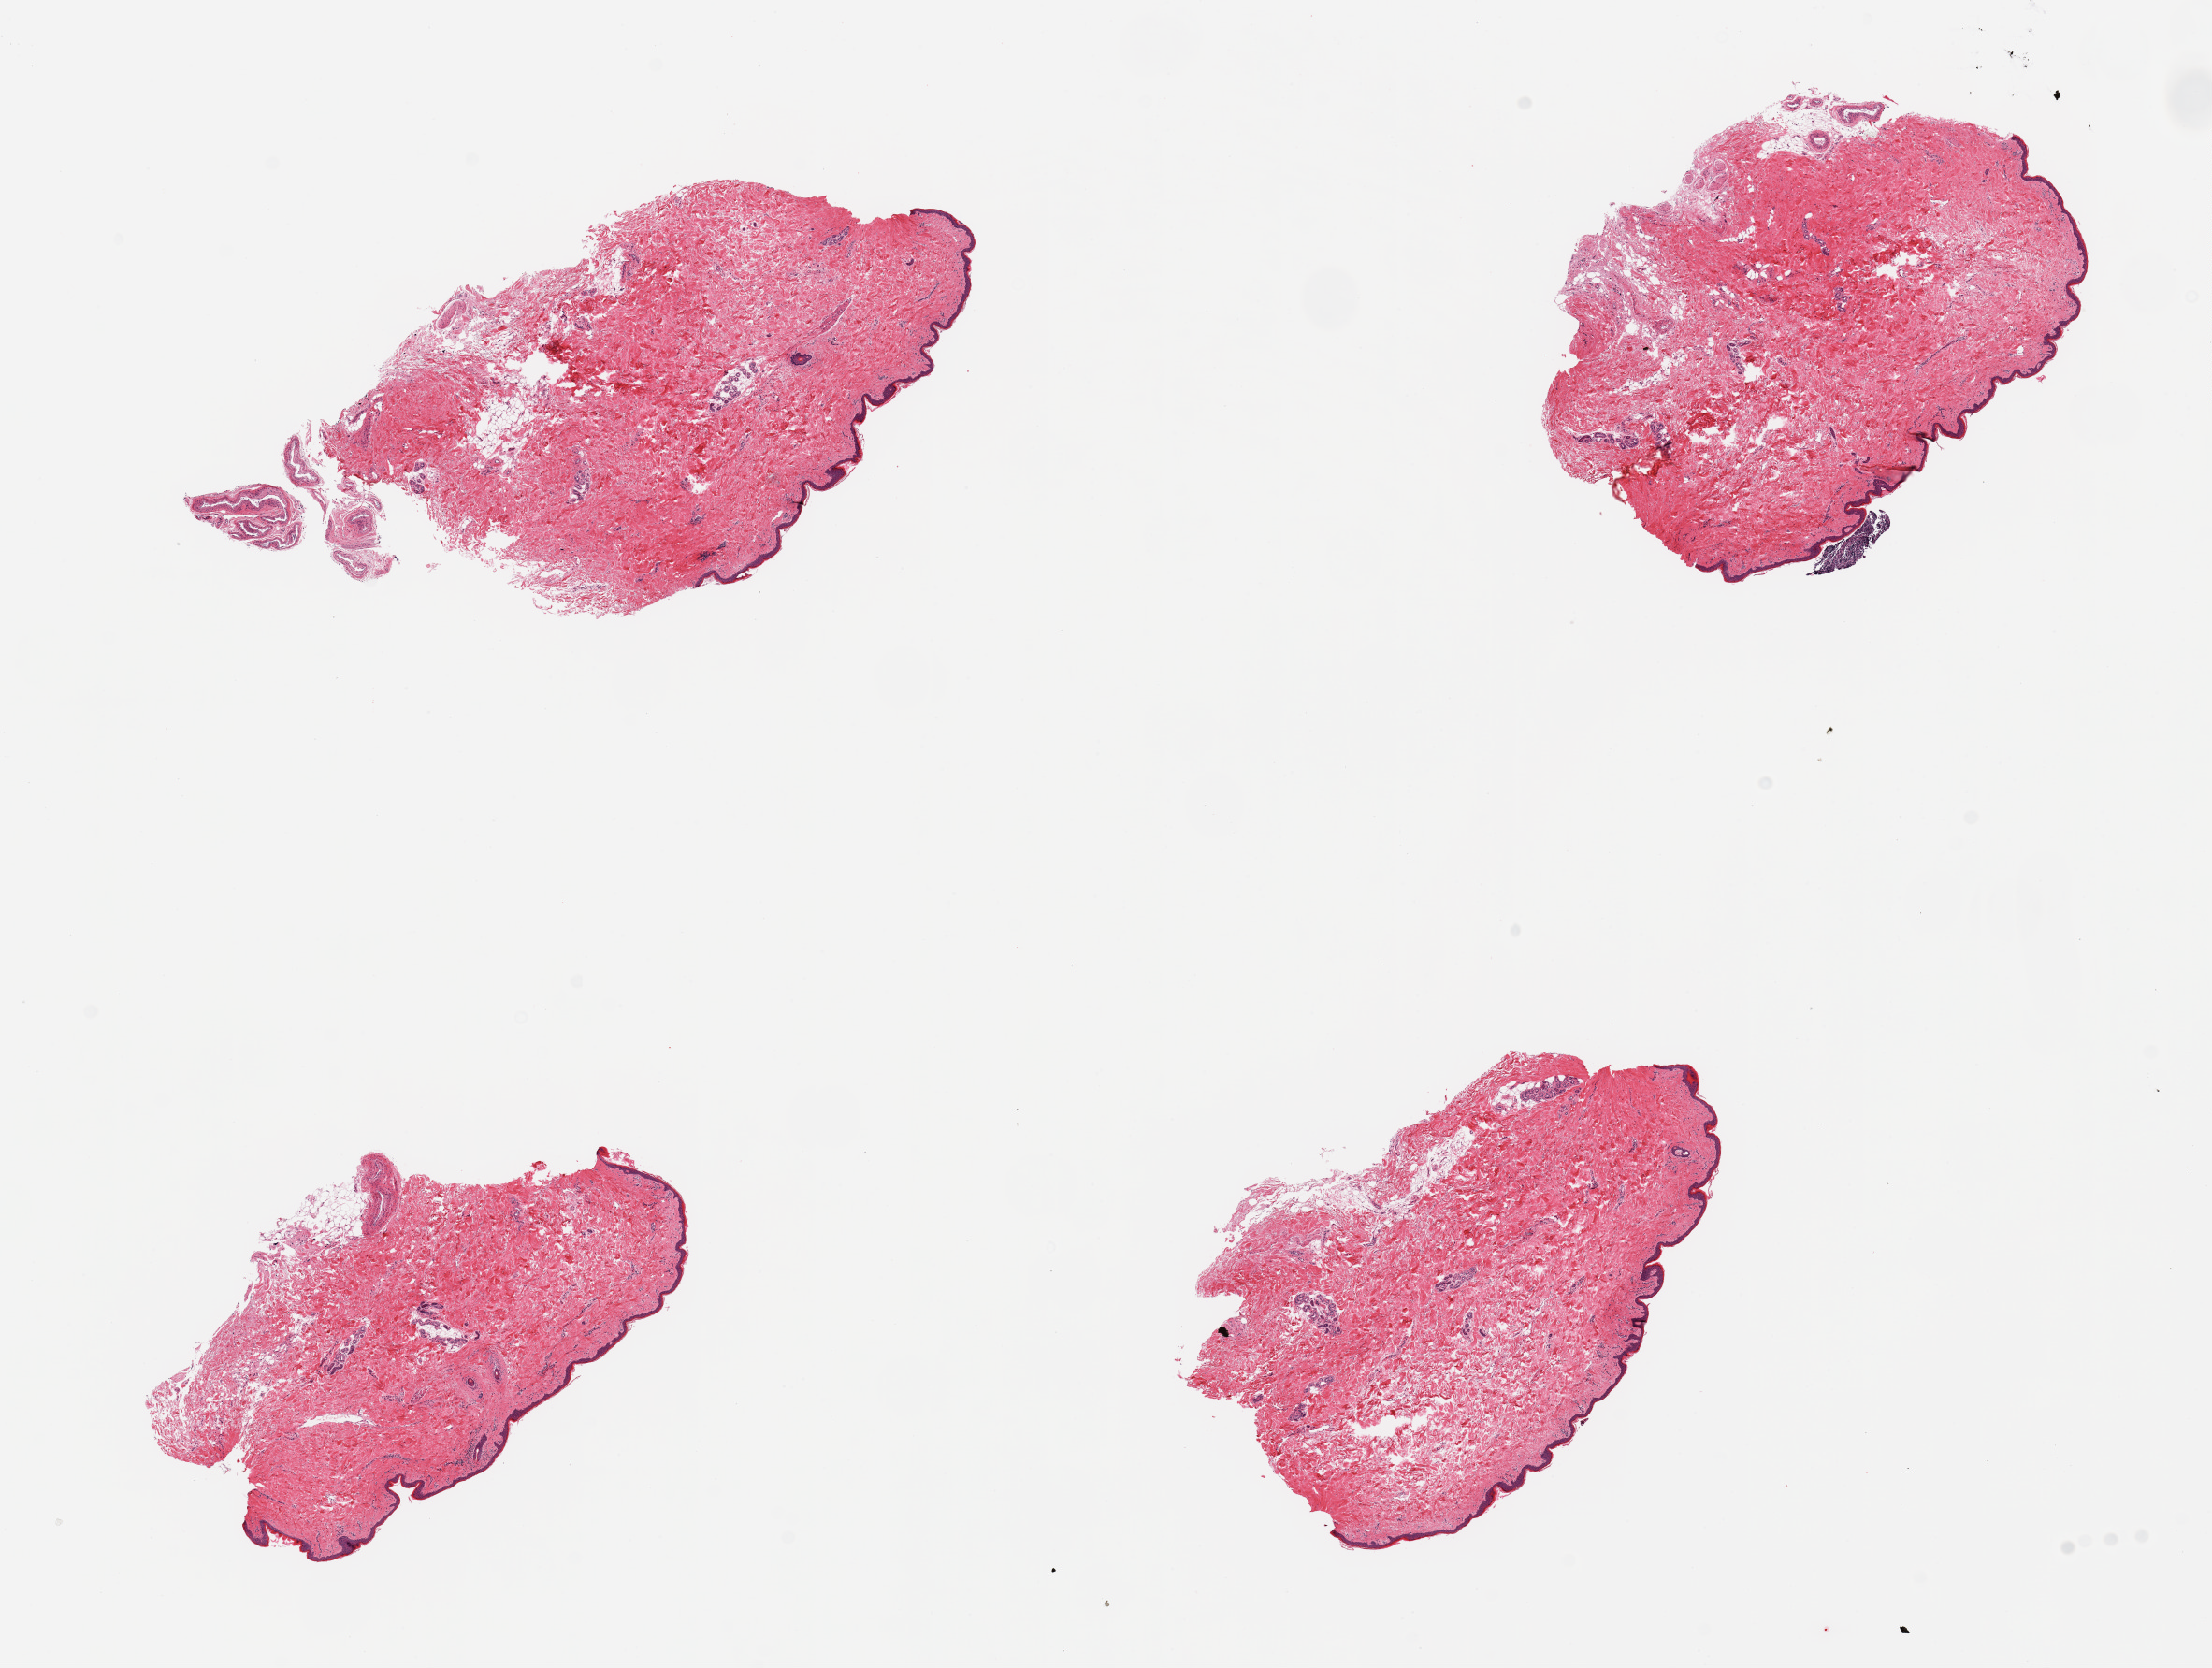
Whole-slide image, hematoxylin and eosin (H&E) stain, brightfield — a low-resolution overview of the entire scanned area, about 18.7 x 14.1 mm (from a 20x scan), PAXgene-fixed paraffin-embedded (PFPE) section, sampled site (target tissue): skin of suprapubic region, tissue donor sample. Female donor.
* reviewer comment on this tissue sample: 4 pieces; well trimmed; <5% intradermal fat; focus of lymphoid carry-over artifact